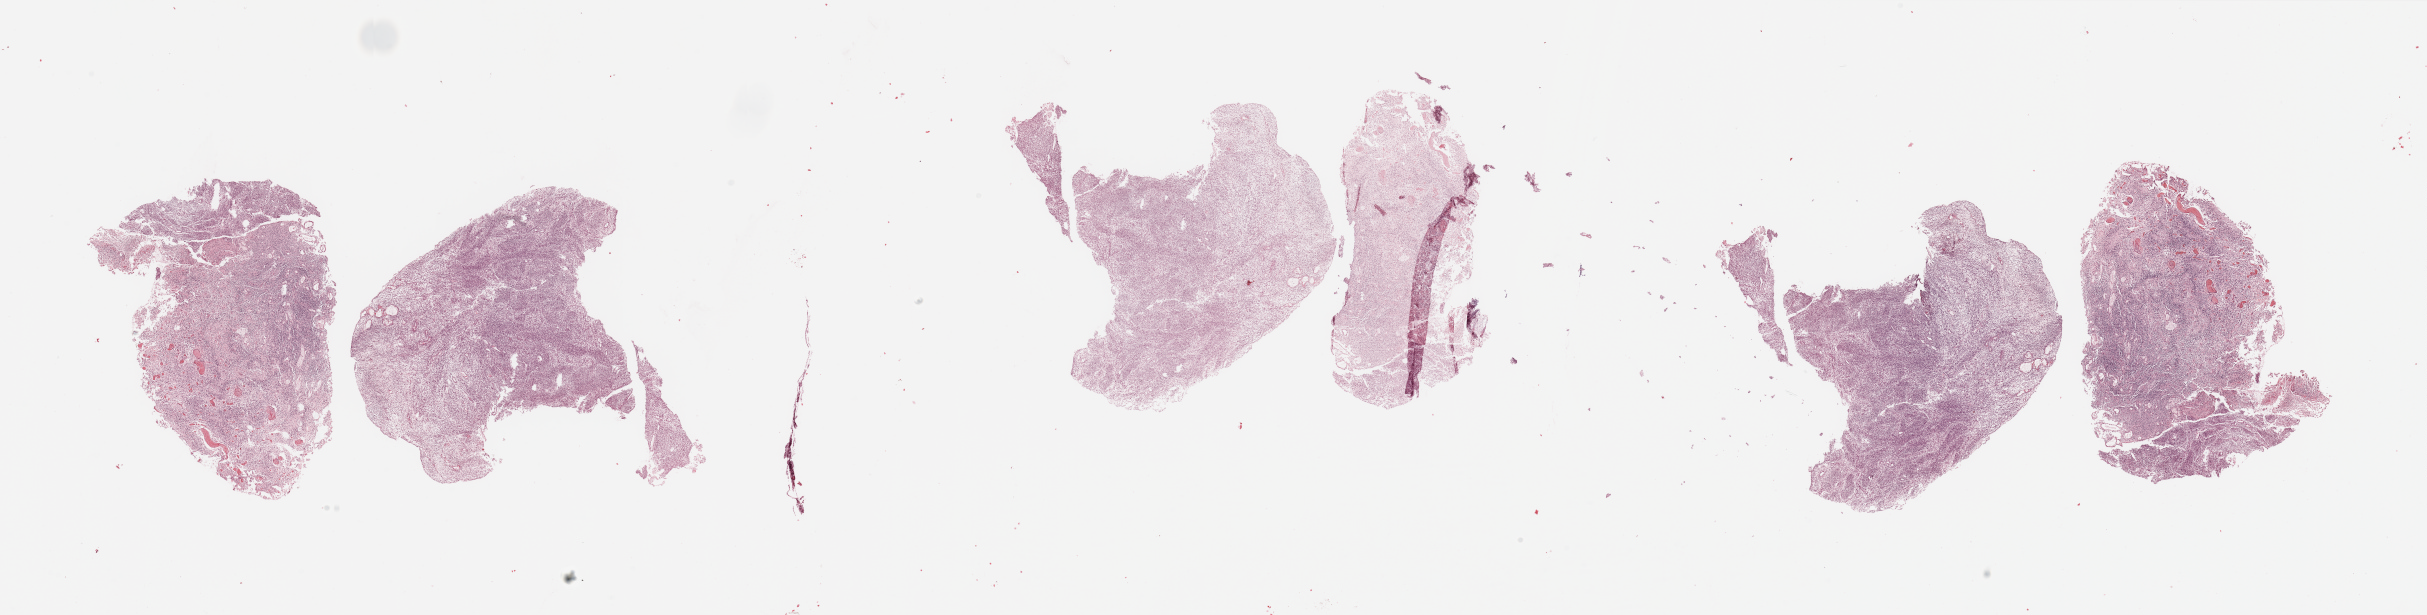
Whole-slide histology image, H&E — low-resolution overview of the scanned area, about 38.4 x 9.7 mm (slide scanned at 20x). Tumour tissue sample, sampled site: frontal lobe. Male, 40 y/o. Slide review estimates, as recorded: tumour nuclei 90%, necrosis 2%.
Histologic diagnosis: Glioblastoma. Primary tumour site (as recorded): frontal lobe.